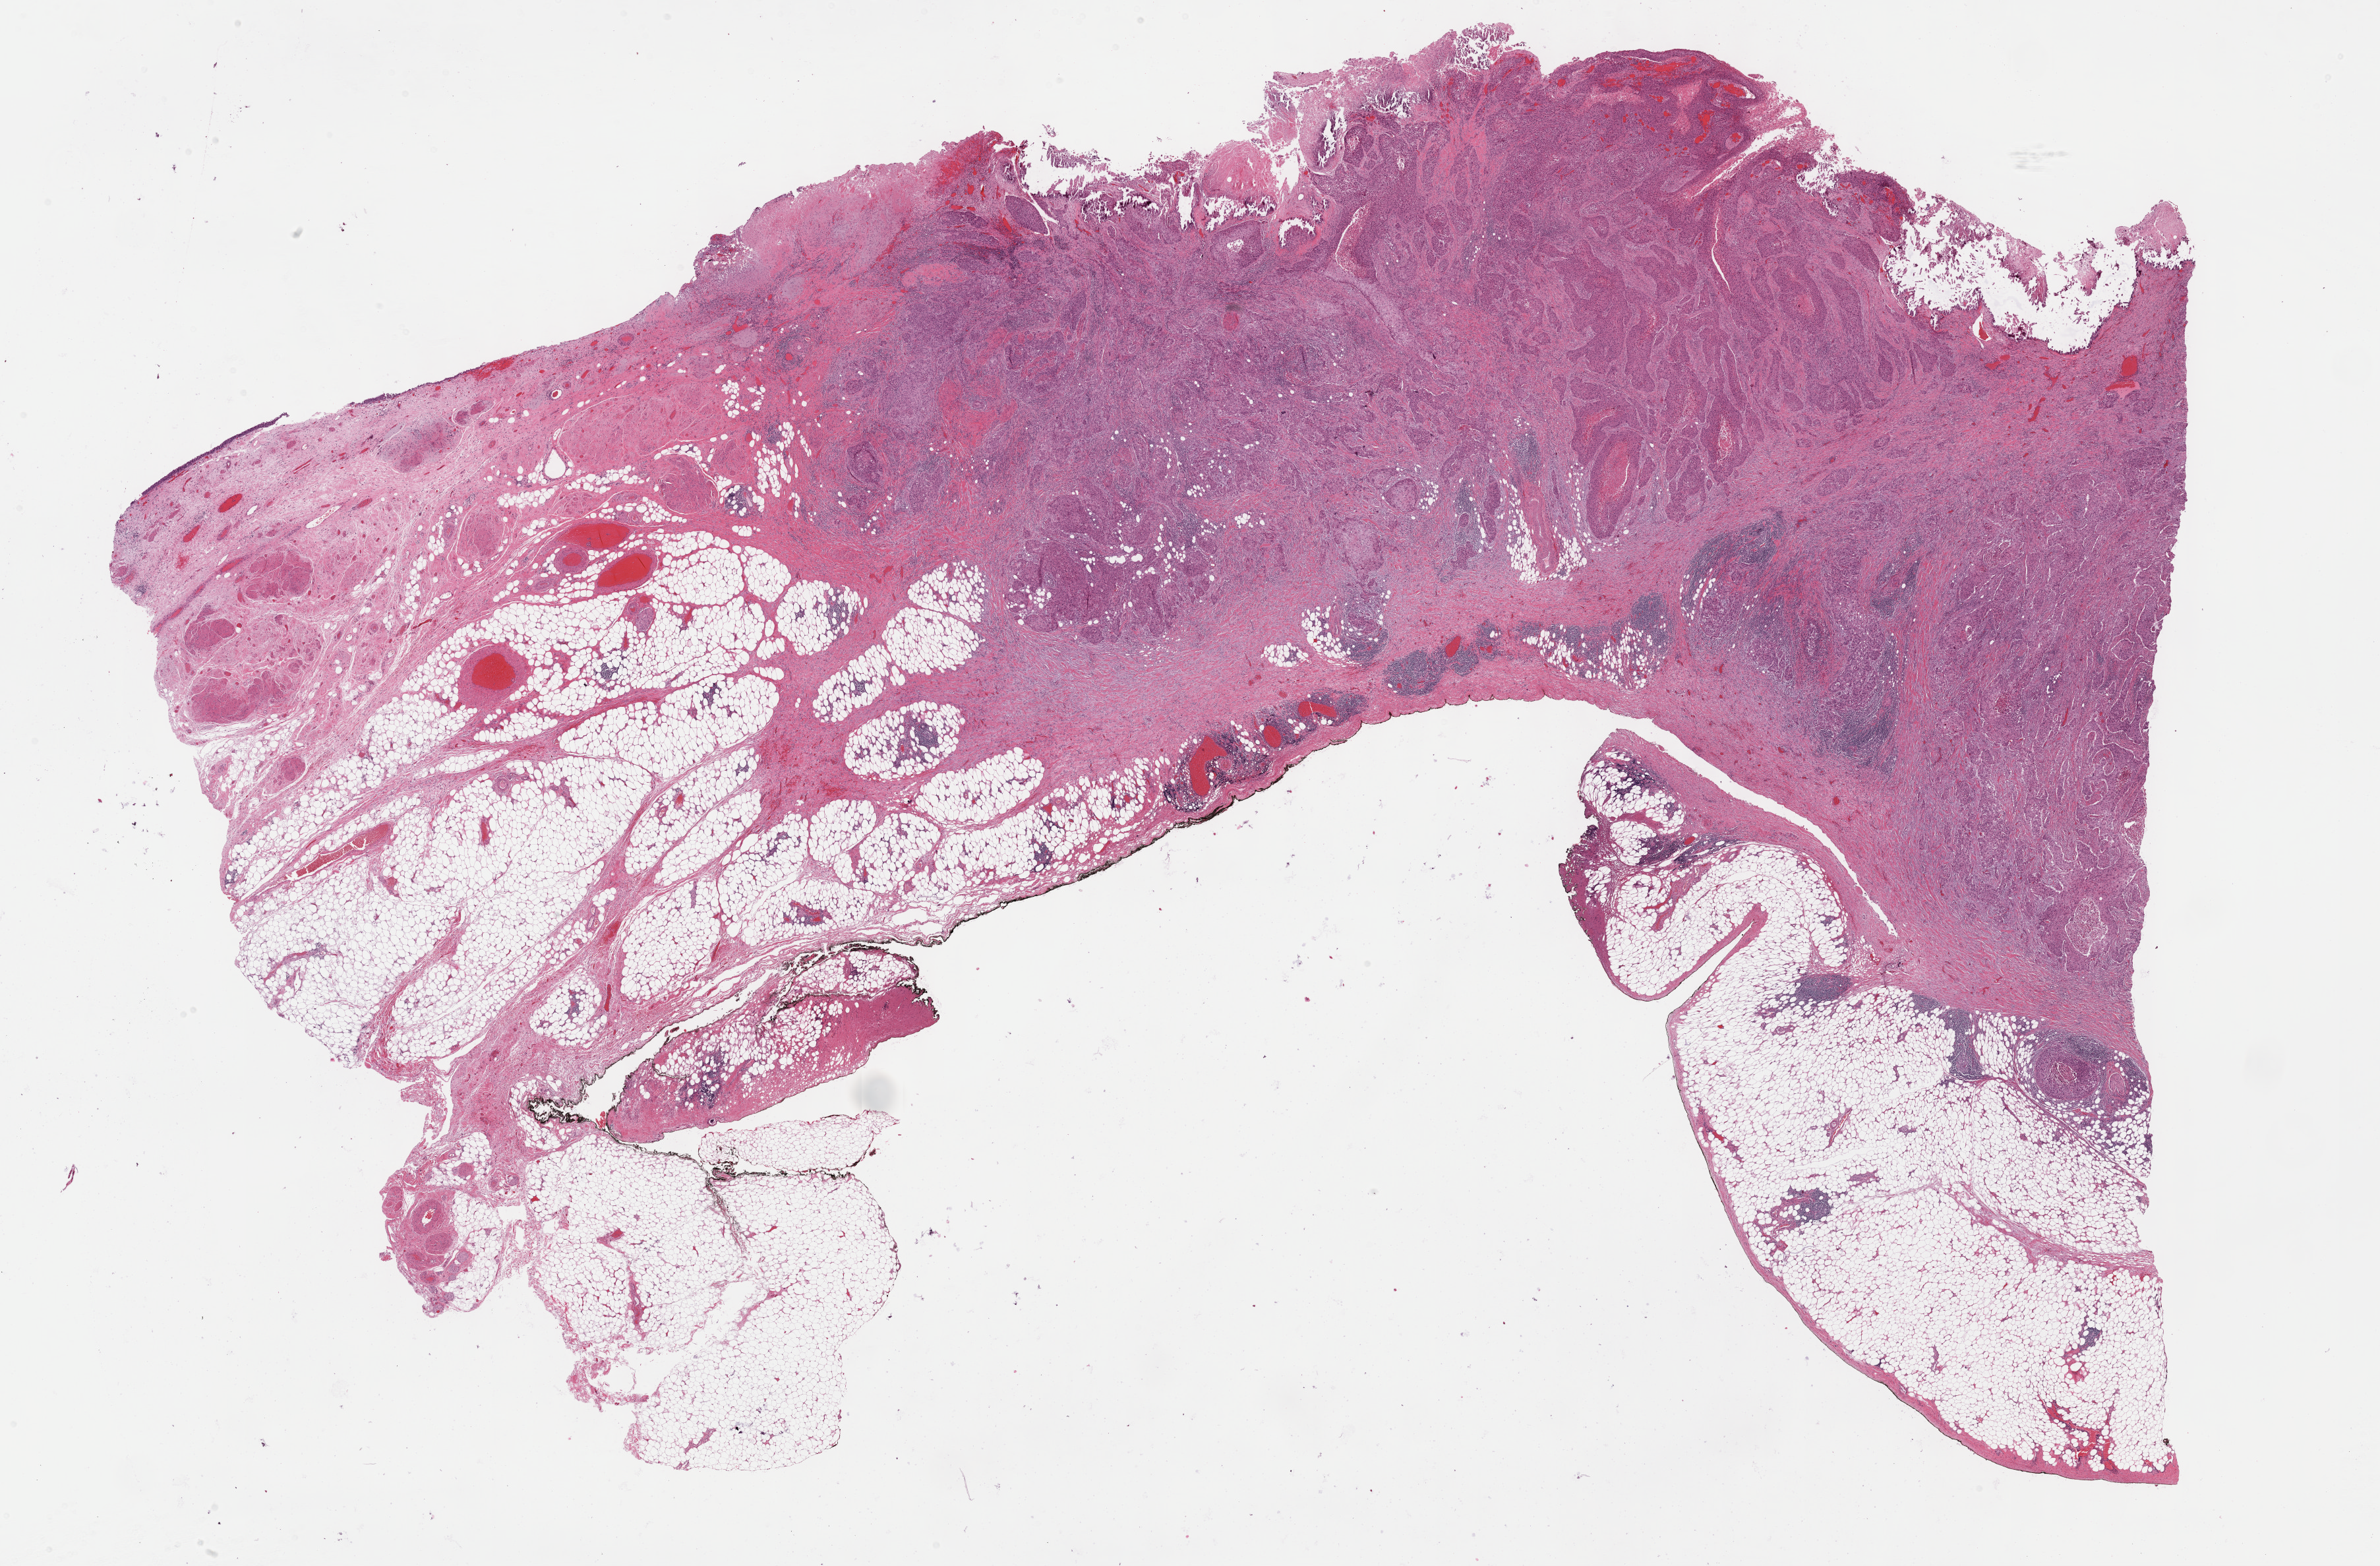
Whole-slide histology image, Hematoxylin and eosin (H&E) stained, shown as a low-resolution overview of the whole scanned area (about 29.2 x 19.2 mm, slide scanned at 40x); formalin-fixed paraffin-embedded (FFPE) diagnostic section; bladder, primary tumour sample. Patient: male, age at initial diagnosis 65 years. Histologic grade: high grade.
Lymph nodes positive (case pathology): 0 of 36 examined. AJCC pathologic stage: III (7th edition). Diagnosis: Transitional cell carcinoma (anterior wall of bladder). TNM: T4 N0 MX.